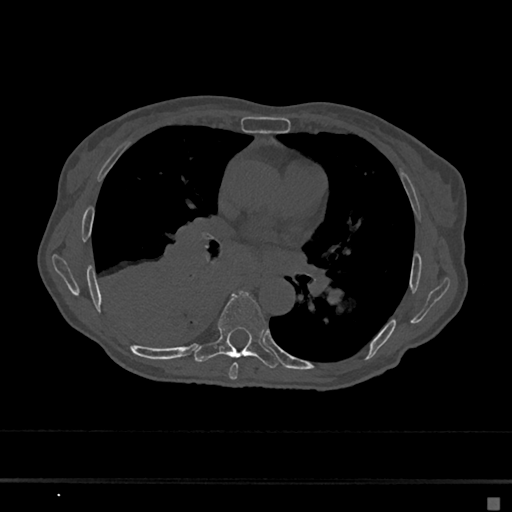
CT including the spine, one axial slice. Reconstruction kernel Br40s/3. Bone window (W 1800 / L 400 HU). 0.5 mm slice thickness. 512 × 512 image matrix, field of view 360 × 360 mm. Female patient, age 68 years. From the clinical record (not read from this slice): primary cancer: renal.
Structures marked on this image (semi-automatically segmented with operator editing):
- T6 vertebra: box from (x=229, y=363) to (x=238, y=380) px
- T7 vertebra: (x=194, y=291)–(x=278, y=368)